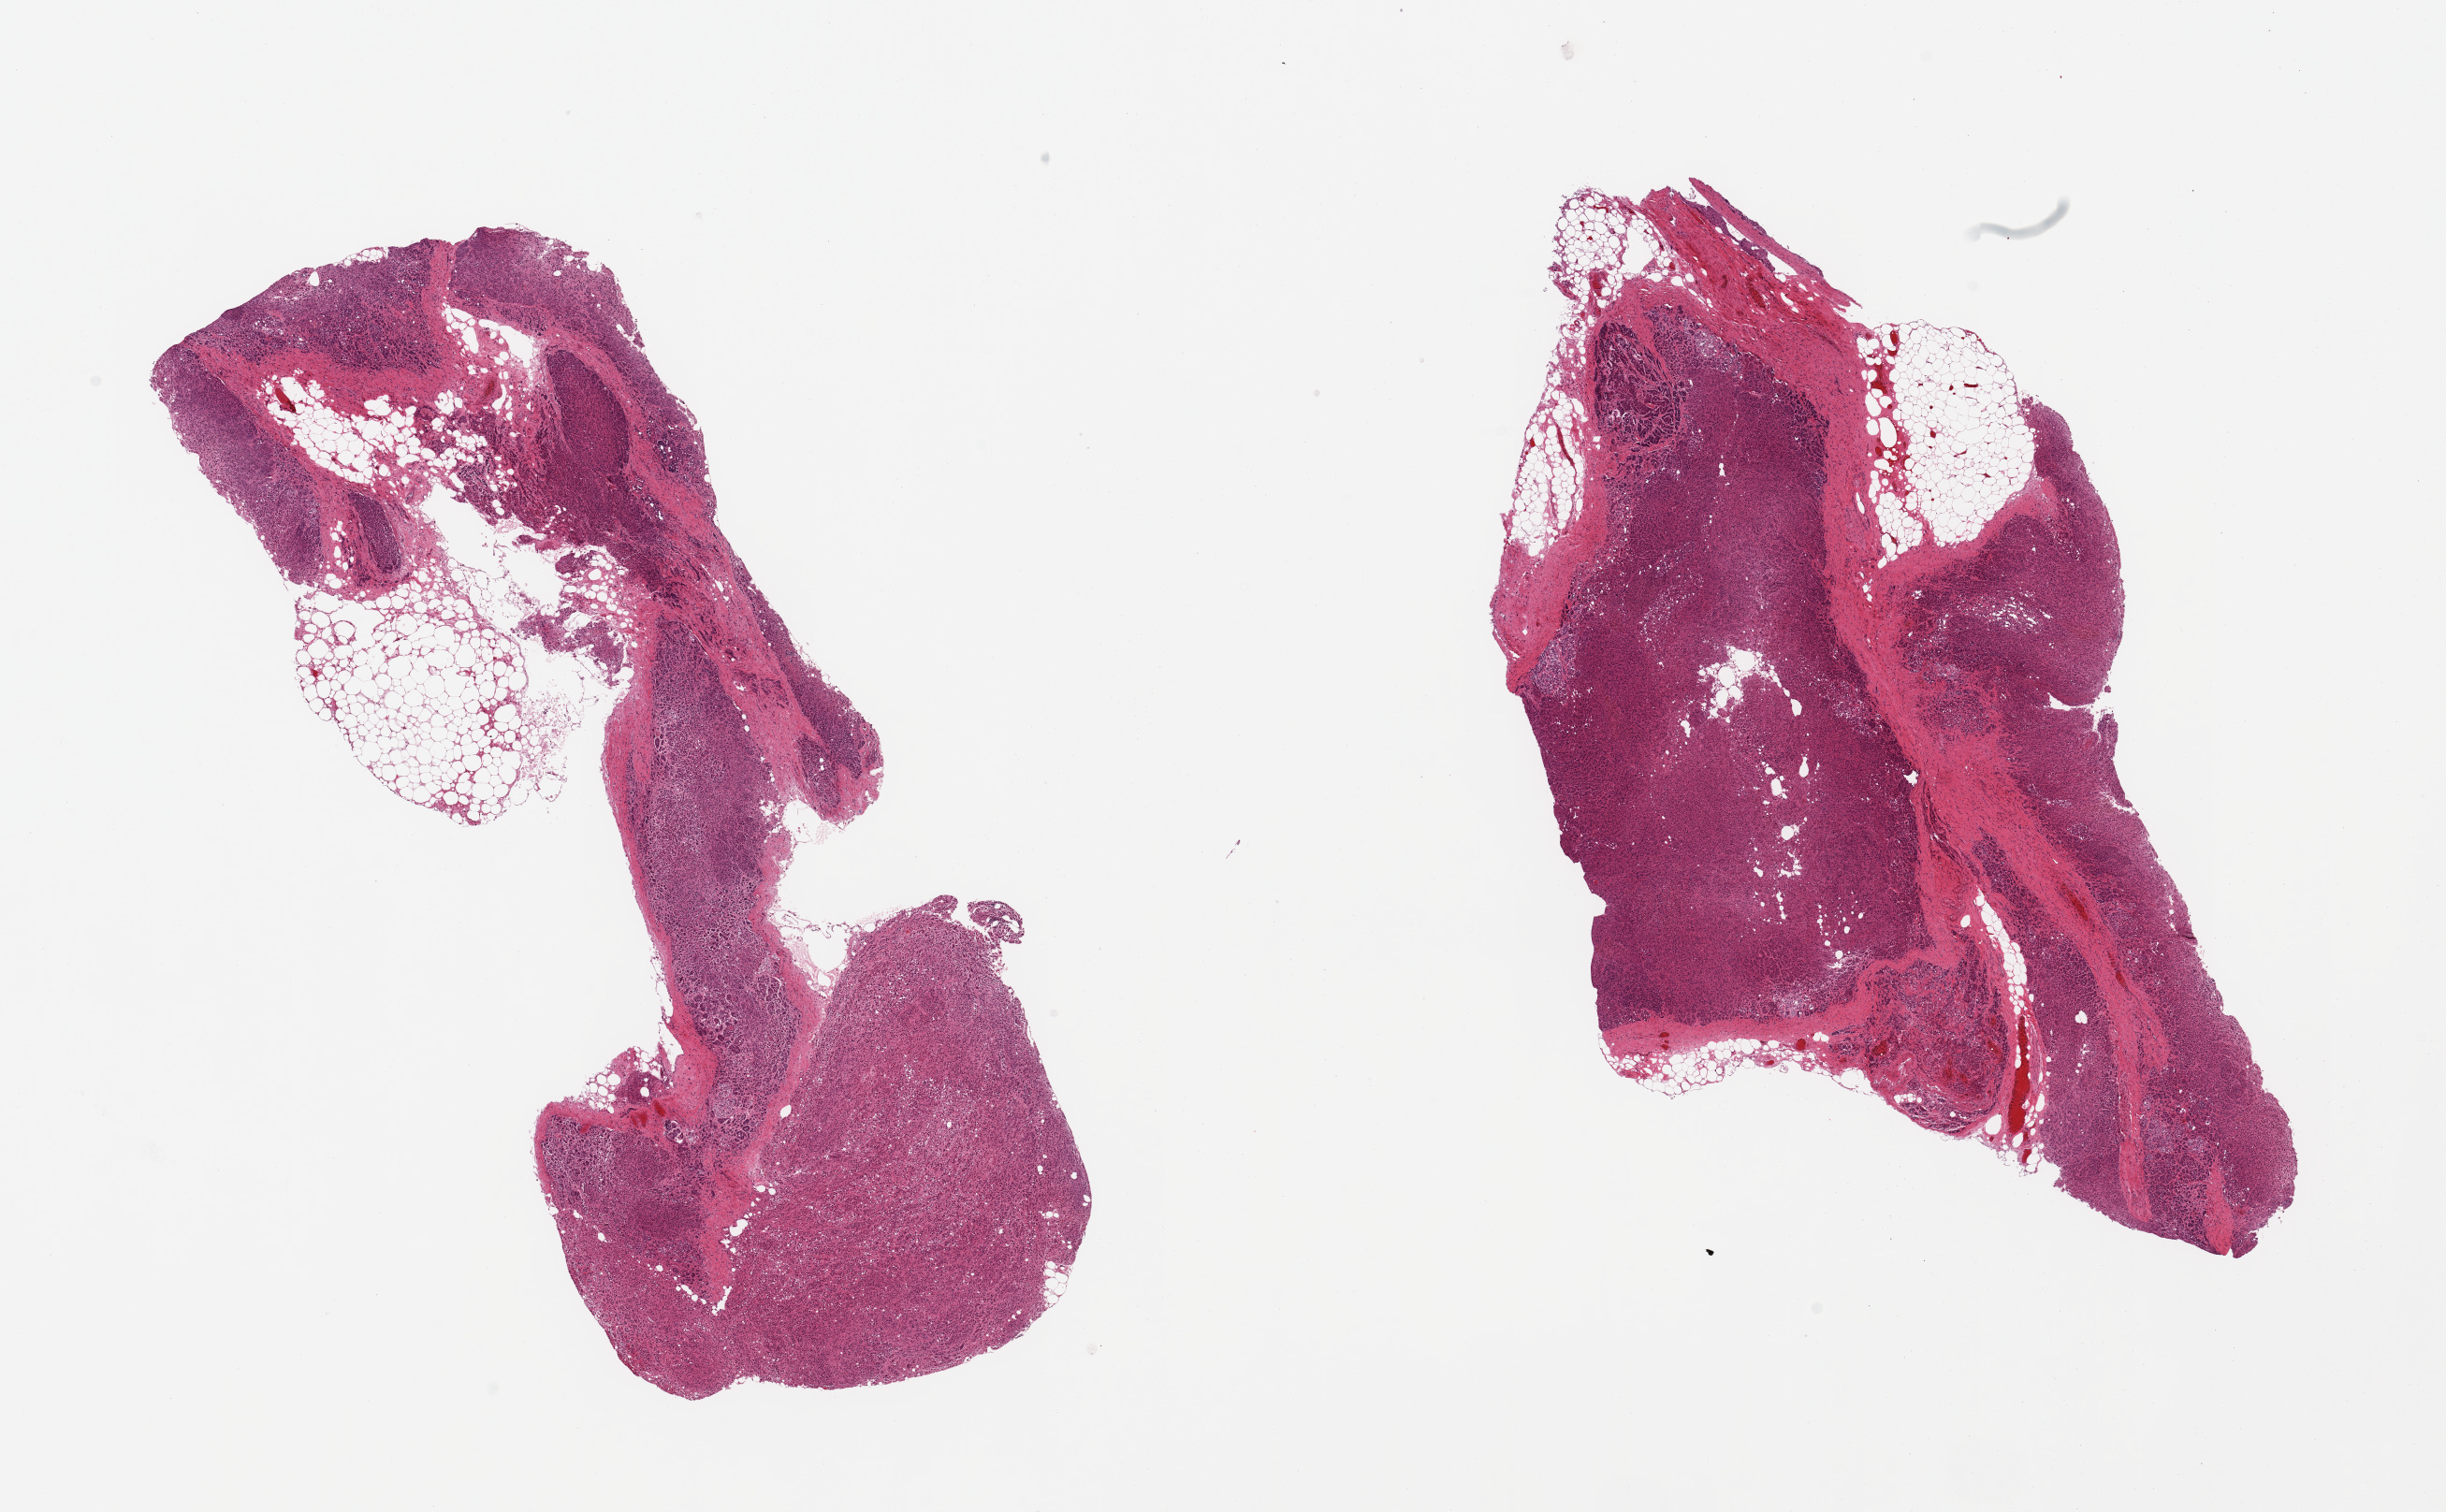
Whole-slide image, haematoxylin and eosin stain, brightfield — a low-resolution overview of the entire scanned area, about 20.7 x 12.8 mm (from a 20x scan), PAXgene-fixed paraffin-embedded (PFPE) section, section of adrenal gland (target tissue), tissue donor sample.
- pathologist's review note for this sample: 2 pieces, ~10% adherent fat, moderately autolyzed cortex